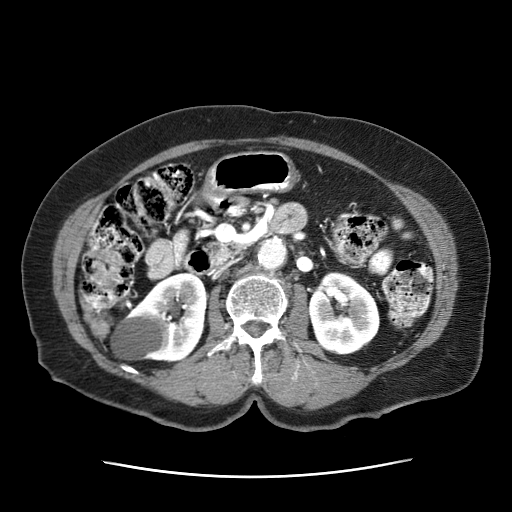
Contrast-enhanced abdominal CT (liver protocol), one axial slice. Position 7 of 63 along the scan axis. Intravenous contrast given. Soft-tissue window (W 400 / L 40 HU). 2.5 mm slice thickness. 512 × 512 image matrix, field of view 360 × 360 mm. Female patient, age 79 years. From the clinical record (not read from this slice): diagnosis: hepatocellular carcinoma (patient treated with transarterial chemoembolisation; whether this scan precedes or follows treatment is not stated here); TNM stage (as recorded): Stage-II; Child-Pugh class: B; tumour nodularity: multinodular.
Outlined on this slice (semi-automatic segmentation, software-assisted and operator-edited):
- abdominal aorta: bounding box [x1, y1, x2, y2] px = [257, 237, 289, 269]